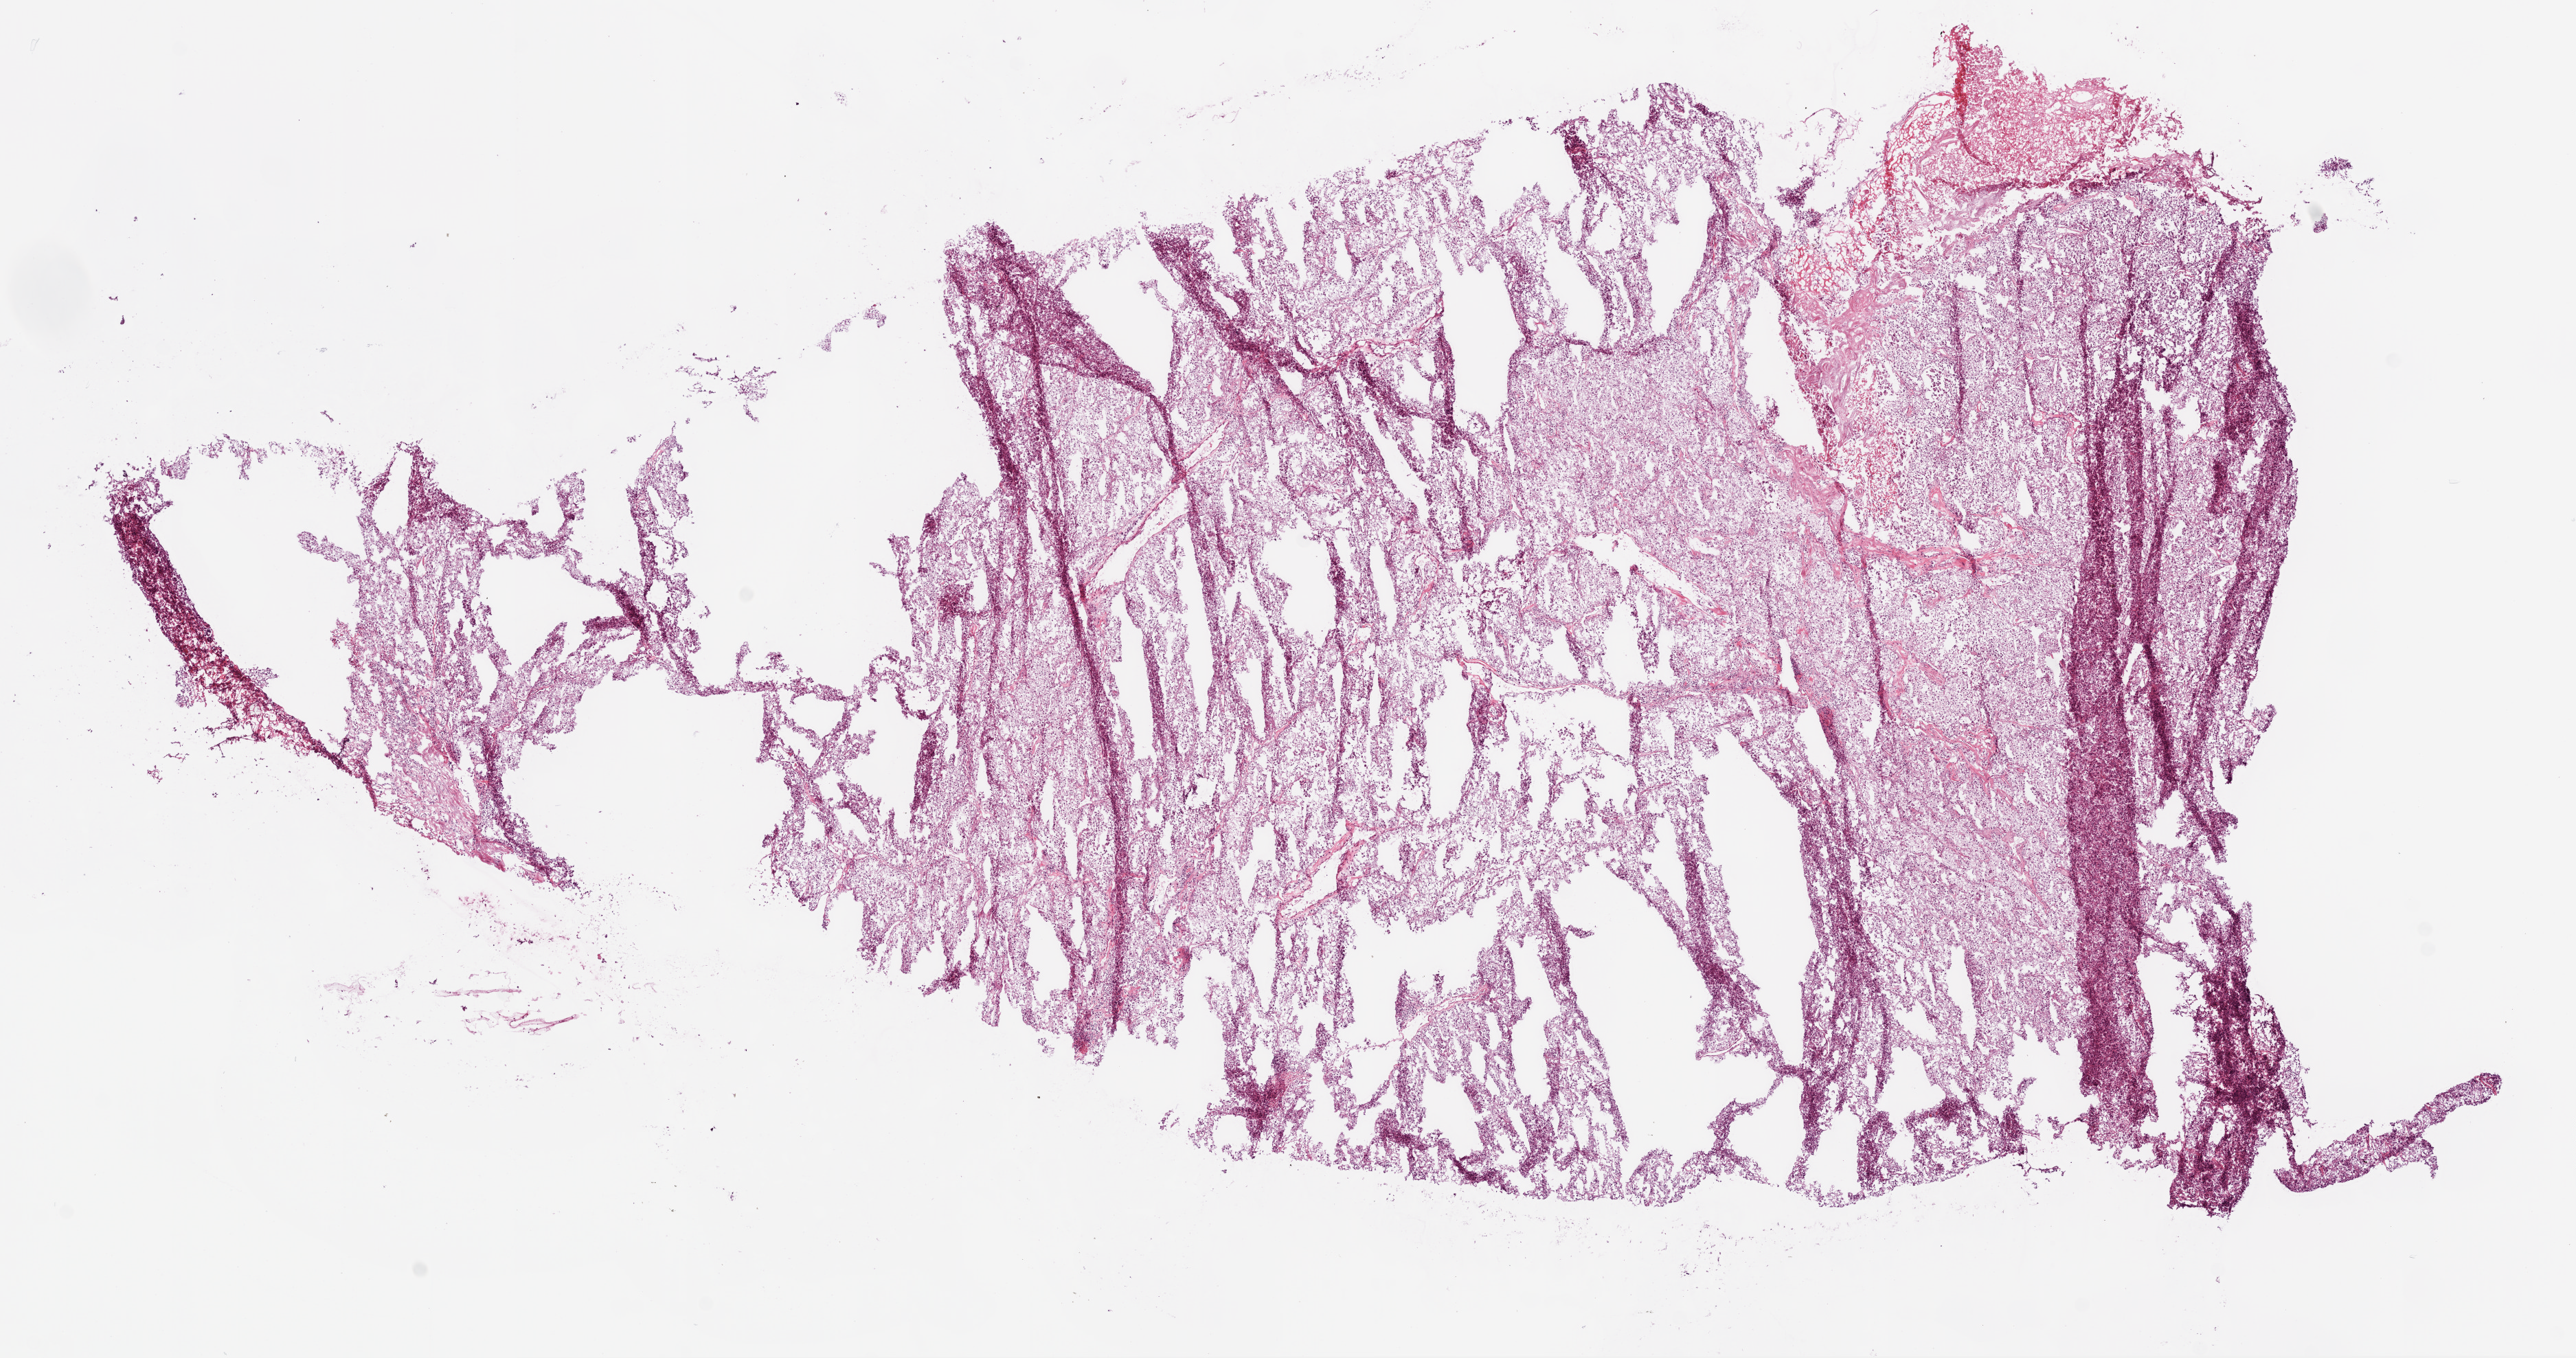
Digitized Hematoxylin and eosin (H&E) stained tissue section (whole slide) — a low-resolution overview of the entire scanned area, about 15.0 x 7.9 mm (acquisition: 20x scan). Frozen section from the bottom of the tissue portion. Kidney, primary tumour sample. Male, age 62 years at initial diagnosis. Histologic grade: G2 (moderately differentiated). Pathologist review of this section (percent, as recorded): tumour cells 82%, tumour nuclei 85%, normal cells 0%, stromal cells 10%, necrosis 8%.
* diagnosis: Clear cell adenocarcinoma, NOS
* laterality: left
* AJCC pathologic stage: IV
* TNM: T3b N0 M1